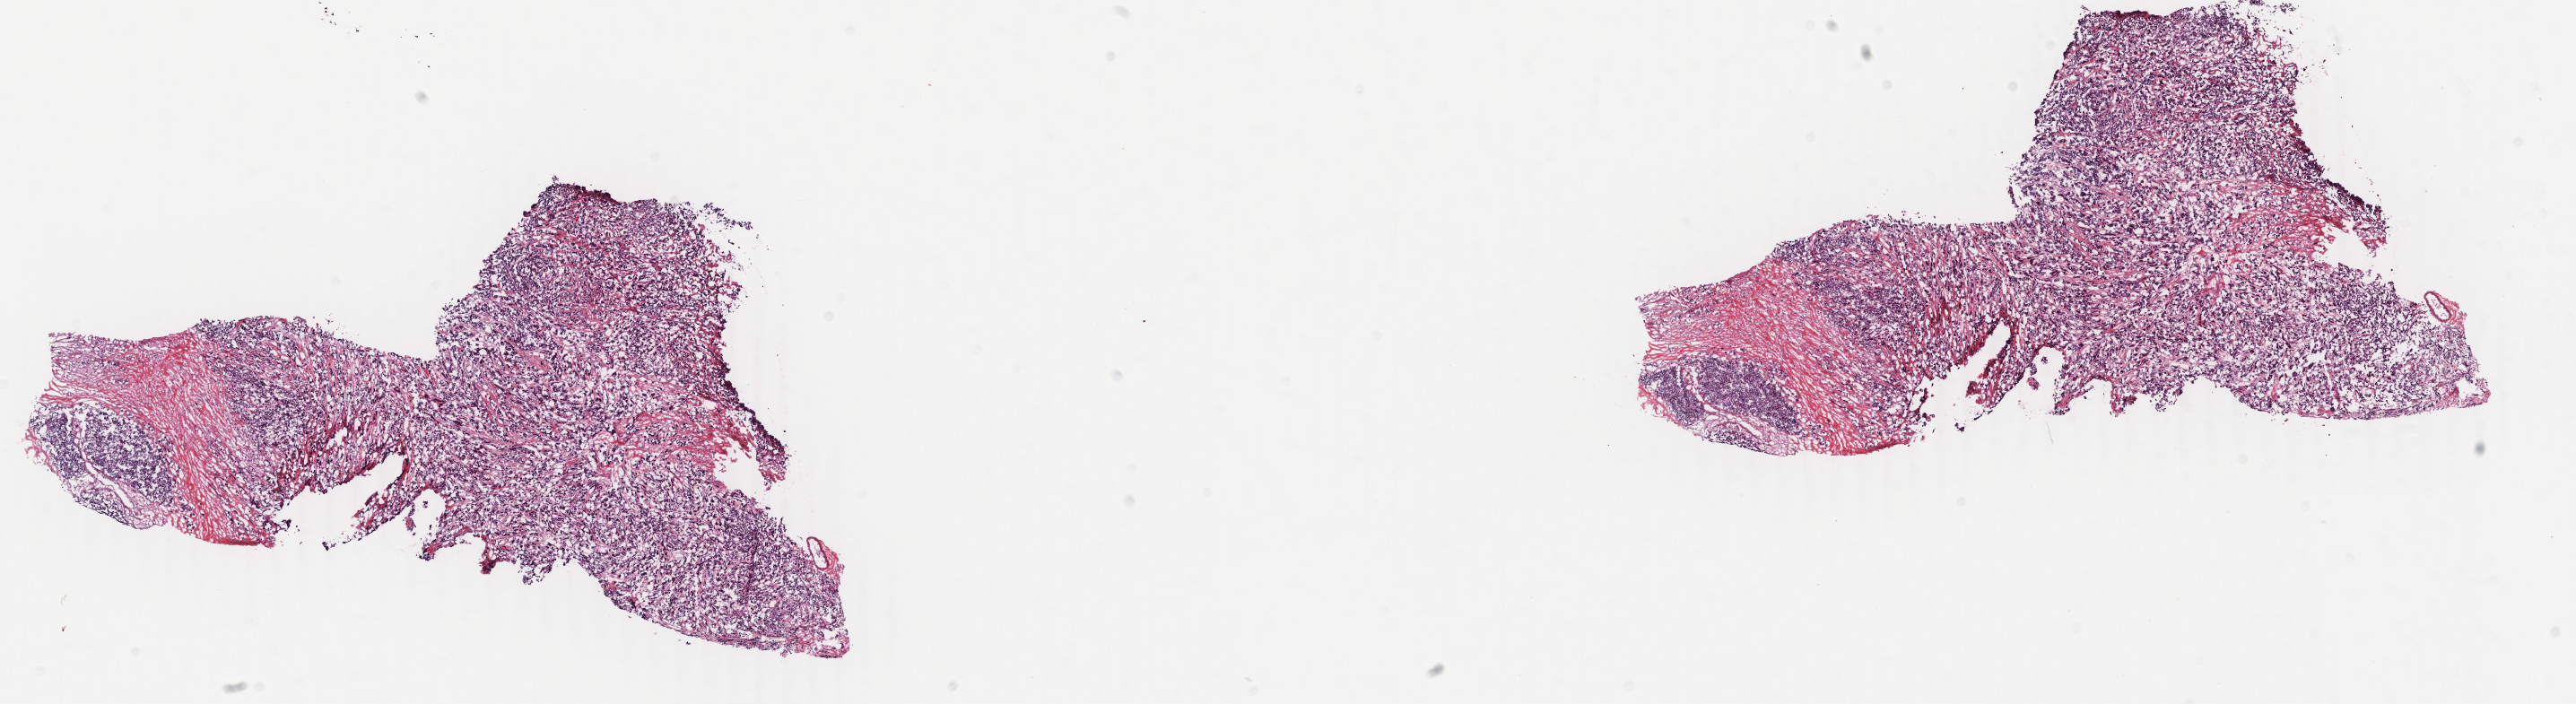
Whole-slide histology image, Hematoxylin and eosin (H&E) stained — a low-resolution overview of the entire scanned area, about 22.8 x 6.2 mm (slide scanned at 40x), frozen section, breast, primary tumour sample. Patient: female, age at initial diagnosis 61 years.
Pathologic diagnosis: Infiltrating duct carcinoma, NOS.